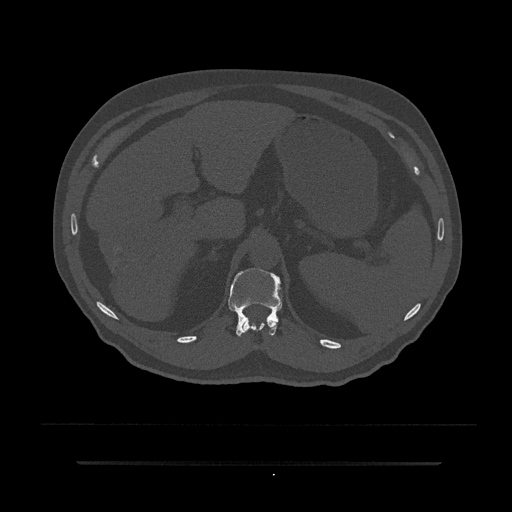
CT including the spine, one axial slice. Position 235 of 797 along the scan axis. Reconstruction kernel Br40s/3. 120 kVp. Bone window (W 1800 / L 400 HU). 0.5 mm slice thickness. 512 × 512 image matrix, field of view 464 × 464 mm. Patient: male, 59 years. From the clinical record (not read from this slice): primary cancer: bile ducts; vertebrae with lytic lesions (as recorded): T10.
Structures marked on this image (semi-automatic segmentation, software-assisted and operator-edited):
- T11 vertebra: bounding box (x1, y1, x2, y2) in pixels: (243, 319, 278, 332)
- T12 vertebra: (228, 268, 282, 336)